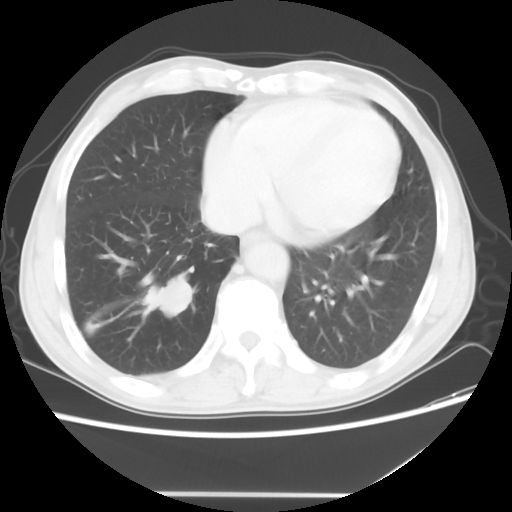
Chest CT, one axial slice. Slice 16 of 56 in the series (ordered by position). 120 kVp. Lung window (W 1500 / L -600 HU). 512 × 512 image matrix, field of view 344 × 344 mm. Patient: male, 65 years. Case-level facts recorded for this patient, not image findings: clinical TNM (as recorded): T1c N3 M0.
Outlined on this slice (bounding box drawn by a radiologist):
- lung tumour (recorded histology: small cell carcinoma): bounding box (x1, y1, x2, y2) in pixels: (141, 268, 196, 319)